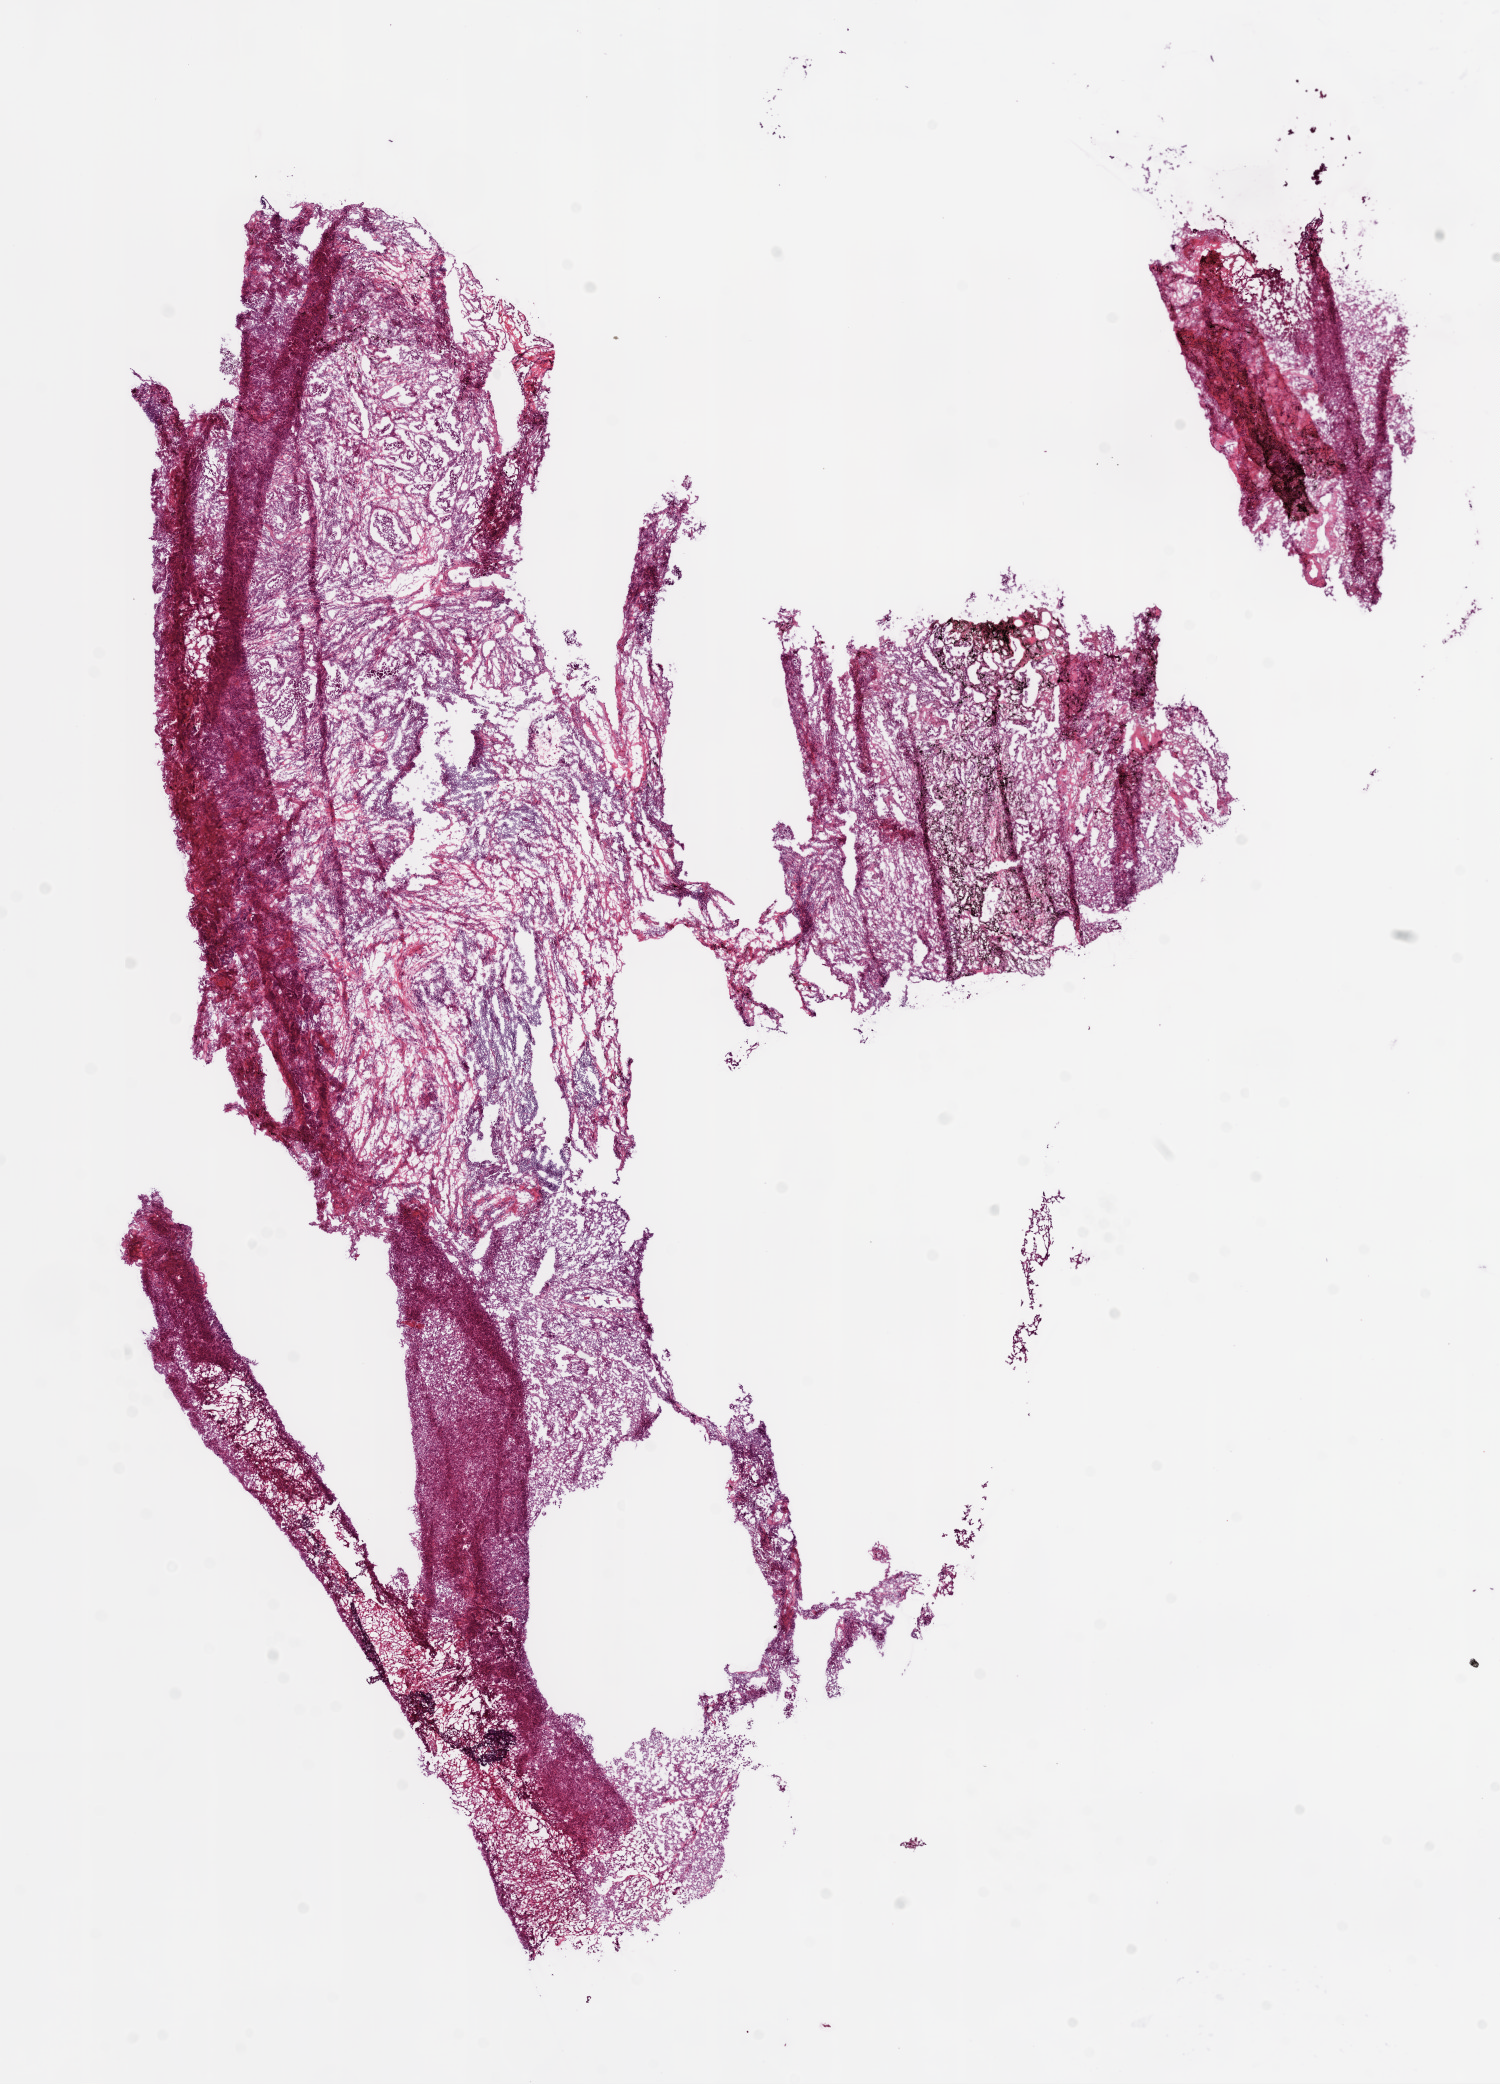
Whole-slide histology image, Hematoxylin and eosin (H&E) stained — shown as a low-resolution overview of the whole scanned area (about 12.0 x 16.7 mm, from a 20x scan). Frozen section. Primary tumour sample from the lung. Male patient; age at initial diagnosis 72 years. Composition of this section per pathologist review: tumour cells 85%, tumour nuclei 60%, normal cells 0%, stromal cells 15%, necrosis 0%.
• AJCC pathologic stage: IB (6th edition)
• histologic diagnosis: Adenocarcinoma with mixed subtypes